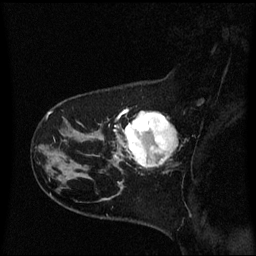
Breast MRI (dynamic contrast-enhanced), one sagittal slice; dynamic contrast-enhanced series, image 2 of 3 at this slice position (ordered by acquisition); 1.5 T; TE 4.2 ms, TR 8.4 ms; 2 mm slice thickness; 256 × 256 image matrix, field of view 220 × 220 mm. Patient: female, 41 years. From the clinical record (not read from this slice): setting: breast cancer imaged before/during neoadjuvant chemotherapy; receptor status: triple-negative.
Outlined on this slice (semi-automatically segmented with operator editing):
- analysis volume of interest (the breast-tissue region the enhancement analysis was run in; not a lesion): bounding box <116,112,177,171> (left, top, right, bottom; pixels)
- tumour enhancement mask (voxels above the 70 % enhancement threshold inside the analysis volume of interest): <116,112,176,167>